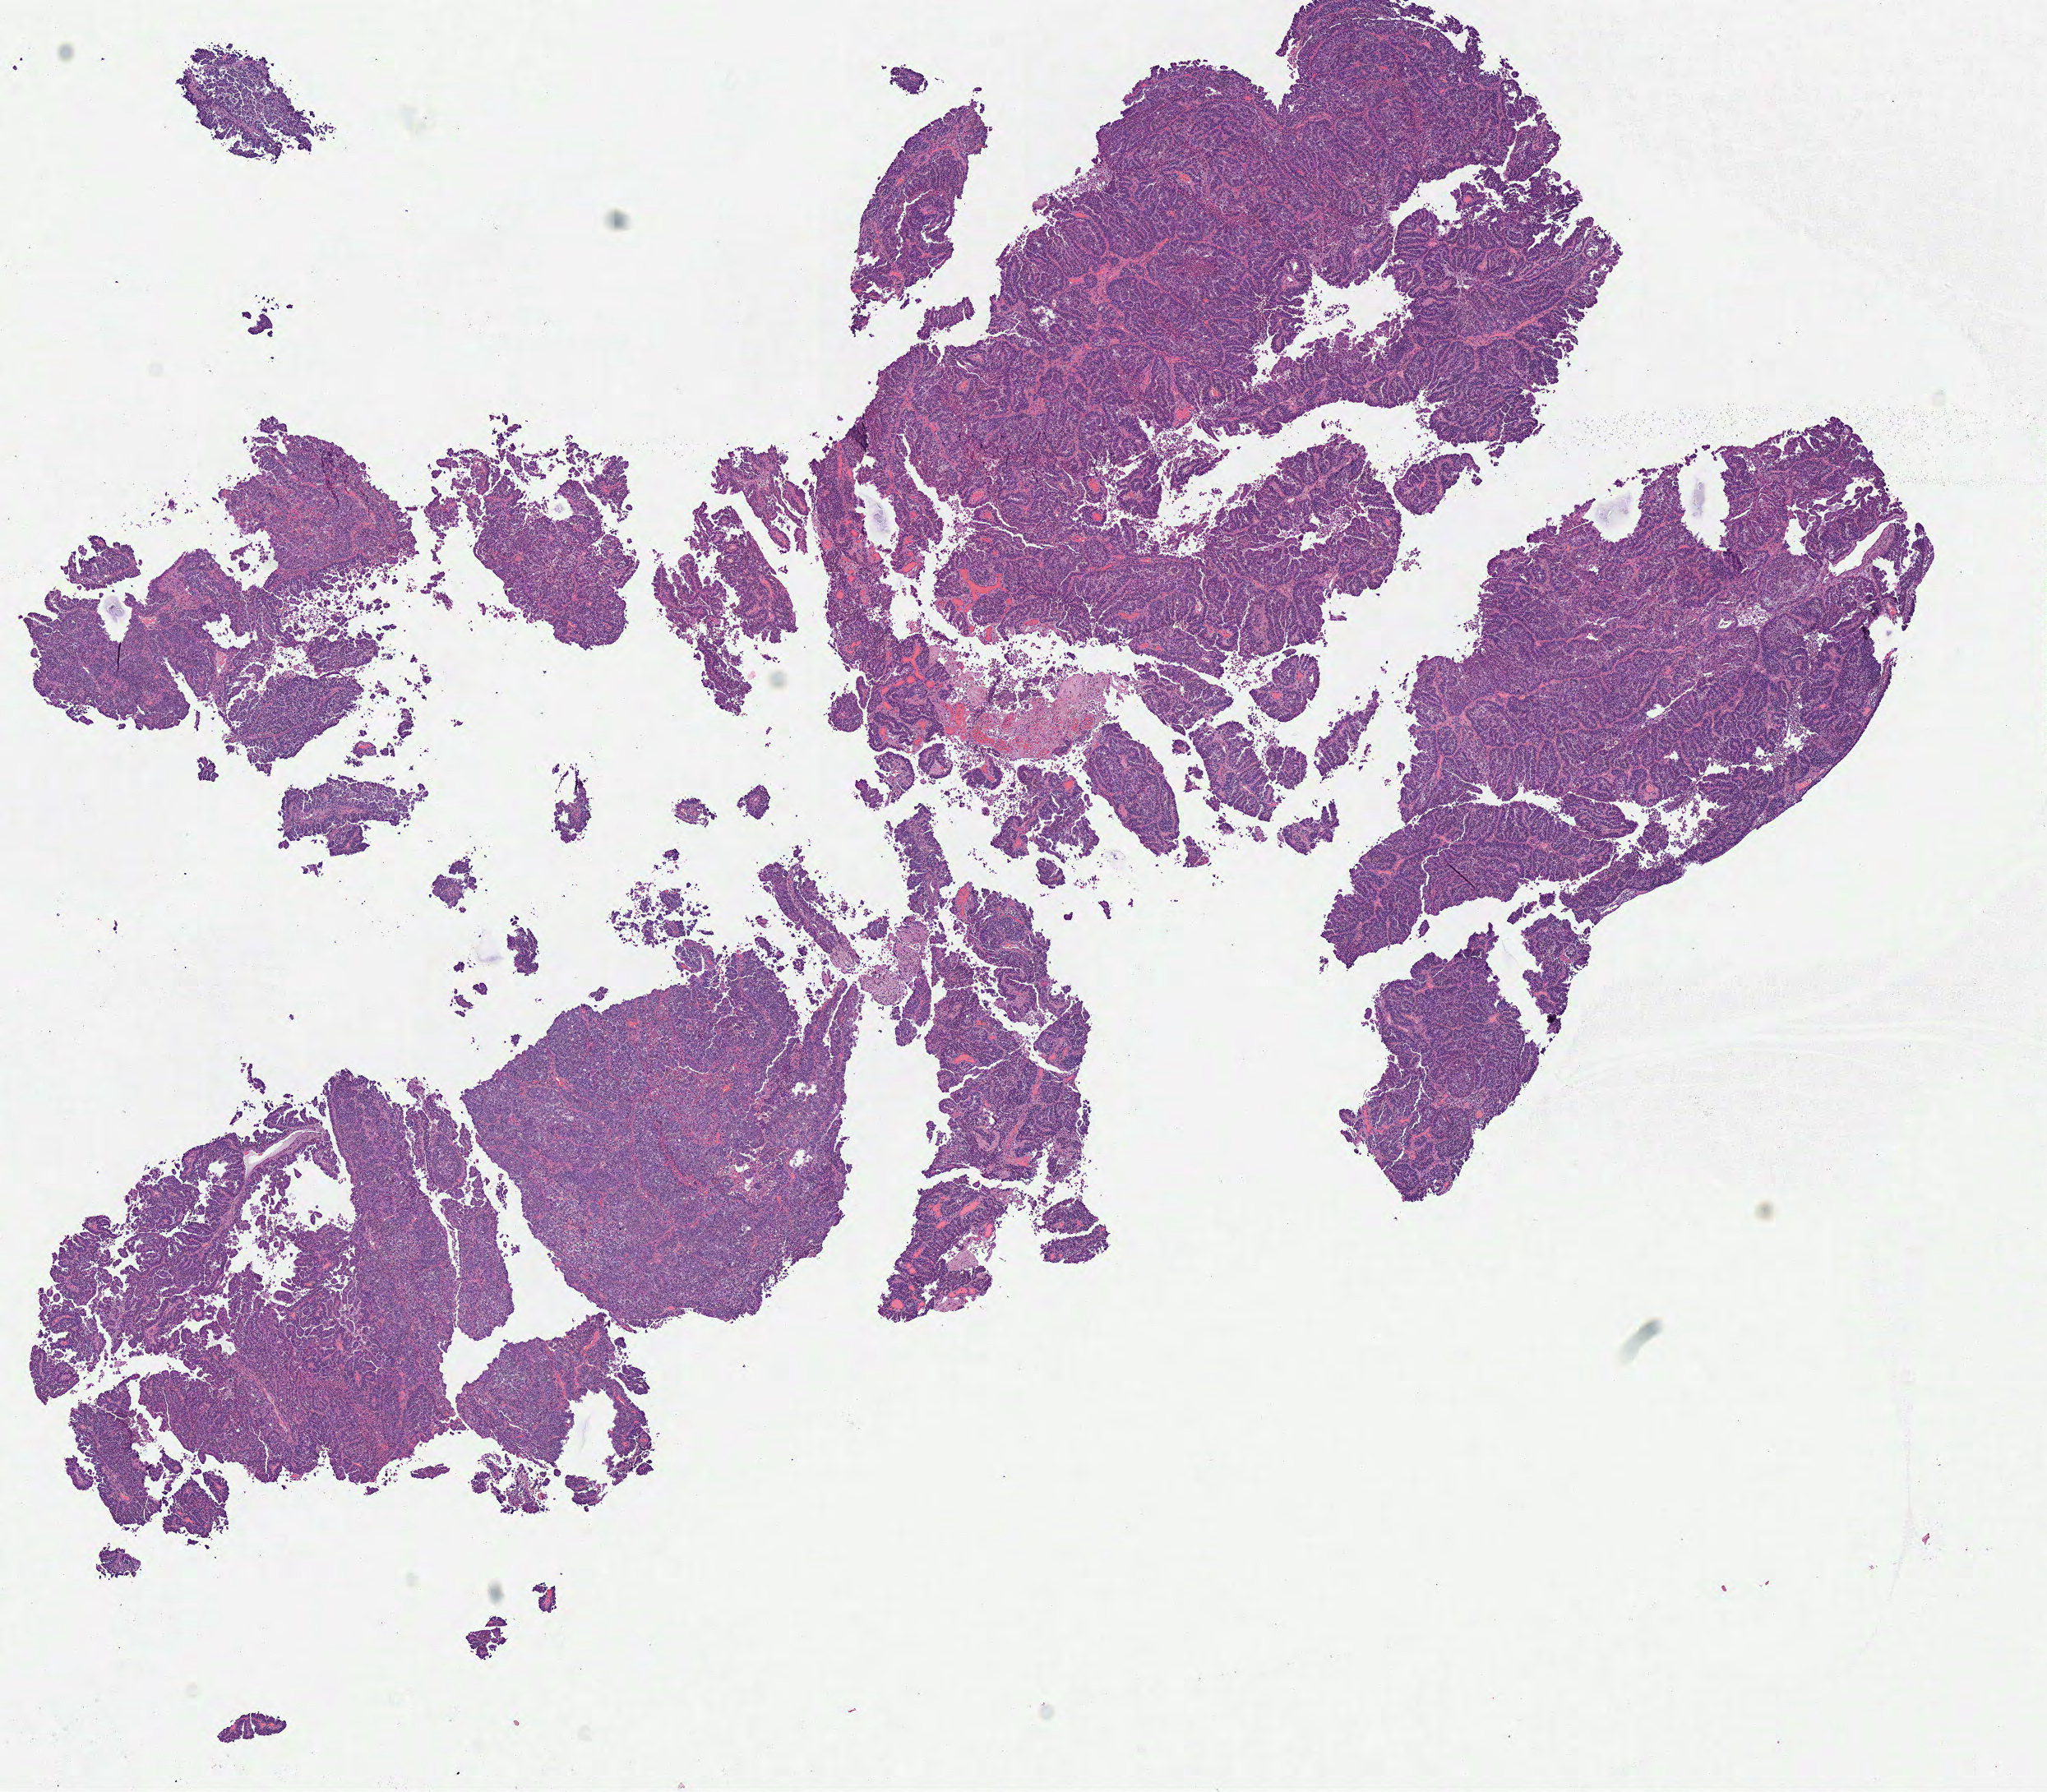
Digitized H&E-stained tissue section (whole slide) — low-resolution overview of the scanned area, about 9.8 x 8.6 mm; formalin-fixed paraffin-embedded (FFPE) diagnostic section; sample: primary tumour, uterus. Patient: female, age at initial diagnosis 61 years. Histologic grade: G3 (poorly differentiated).
* FIGO stage: II
* pathologic diagnosis: Serous cystadenocarcinoma, NOS